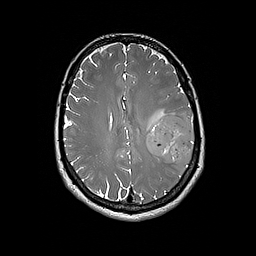
Brain MRI from a brain-tumour surgery series, one axial slice. Slice 78 of 192 in the series (ordered by position). 1 mm slice thickness. 256 × 256 image matrix, field of view 250 × 250 mm. Case-level facts recorded for this patient, not image findings: histopathology: Glioblastoma; WHO grade: 4; IDH mutation: no.
Structures marked on this image (manually delineated by an expert):
- tumour: bounding box [x1, y1, x2, y2] px = [146, 113, 195, 166]